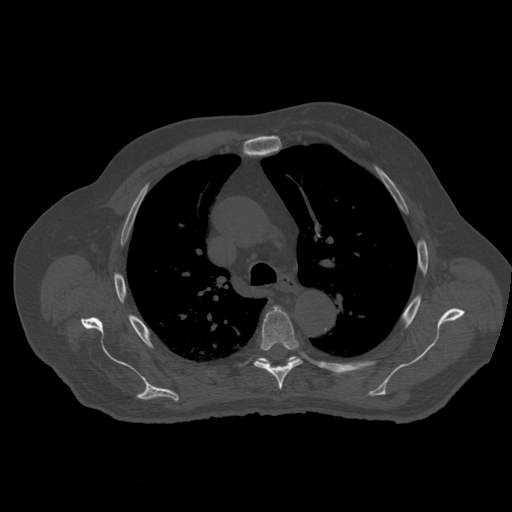
CT including the spine, one axial slice; position 397 of 399 along the scan axis; reconstruction kernel STANDARD; 120 kVp; bone window (W 1800 / L 400 HU); 1.25 mm slice thickness; 512 × 512 image matrix, field of view 407 × 407 mm. Patient age 73 years. From the clinical record (not read from this slice): primary cancer: prostate; vertebrae with lytic lesions (as recorded): L2.
Annotated regions visible in this slice (semi-automatic segmentation, software-assisted and operator-edited):
- T5 vertebra: bounding box <254,307,303,391> (left, top, right, bottom; pixels)
- T6 vertebra: <257,356,299,365>